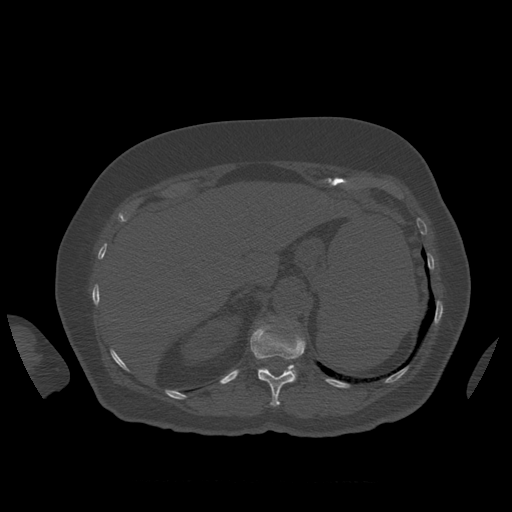
CT including the spine, one axial slice; slice 297 of 399 in the series (ordered by position); reconstruction kernel STANDARD; 120 kVp; bone window (W 1800 / L 400 HU); 1.25 mm slice thickness; 512 × 512 image matrix, field of view 404 × 404 mm. Patient age 81 years. From the clinical record (not read from this slice): primary cancer: renal.
Outlined on this slice (semi-automatic segmentation, software-assisted and operator-edited):
- L1 vertebra: bounding box [x1, y1, x2, y2] px = [293, 365, 298, 376]
- T12 vertebra: [251, 320, 306, 407]